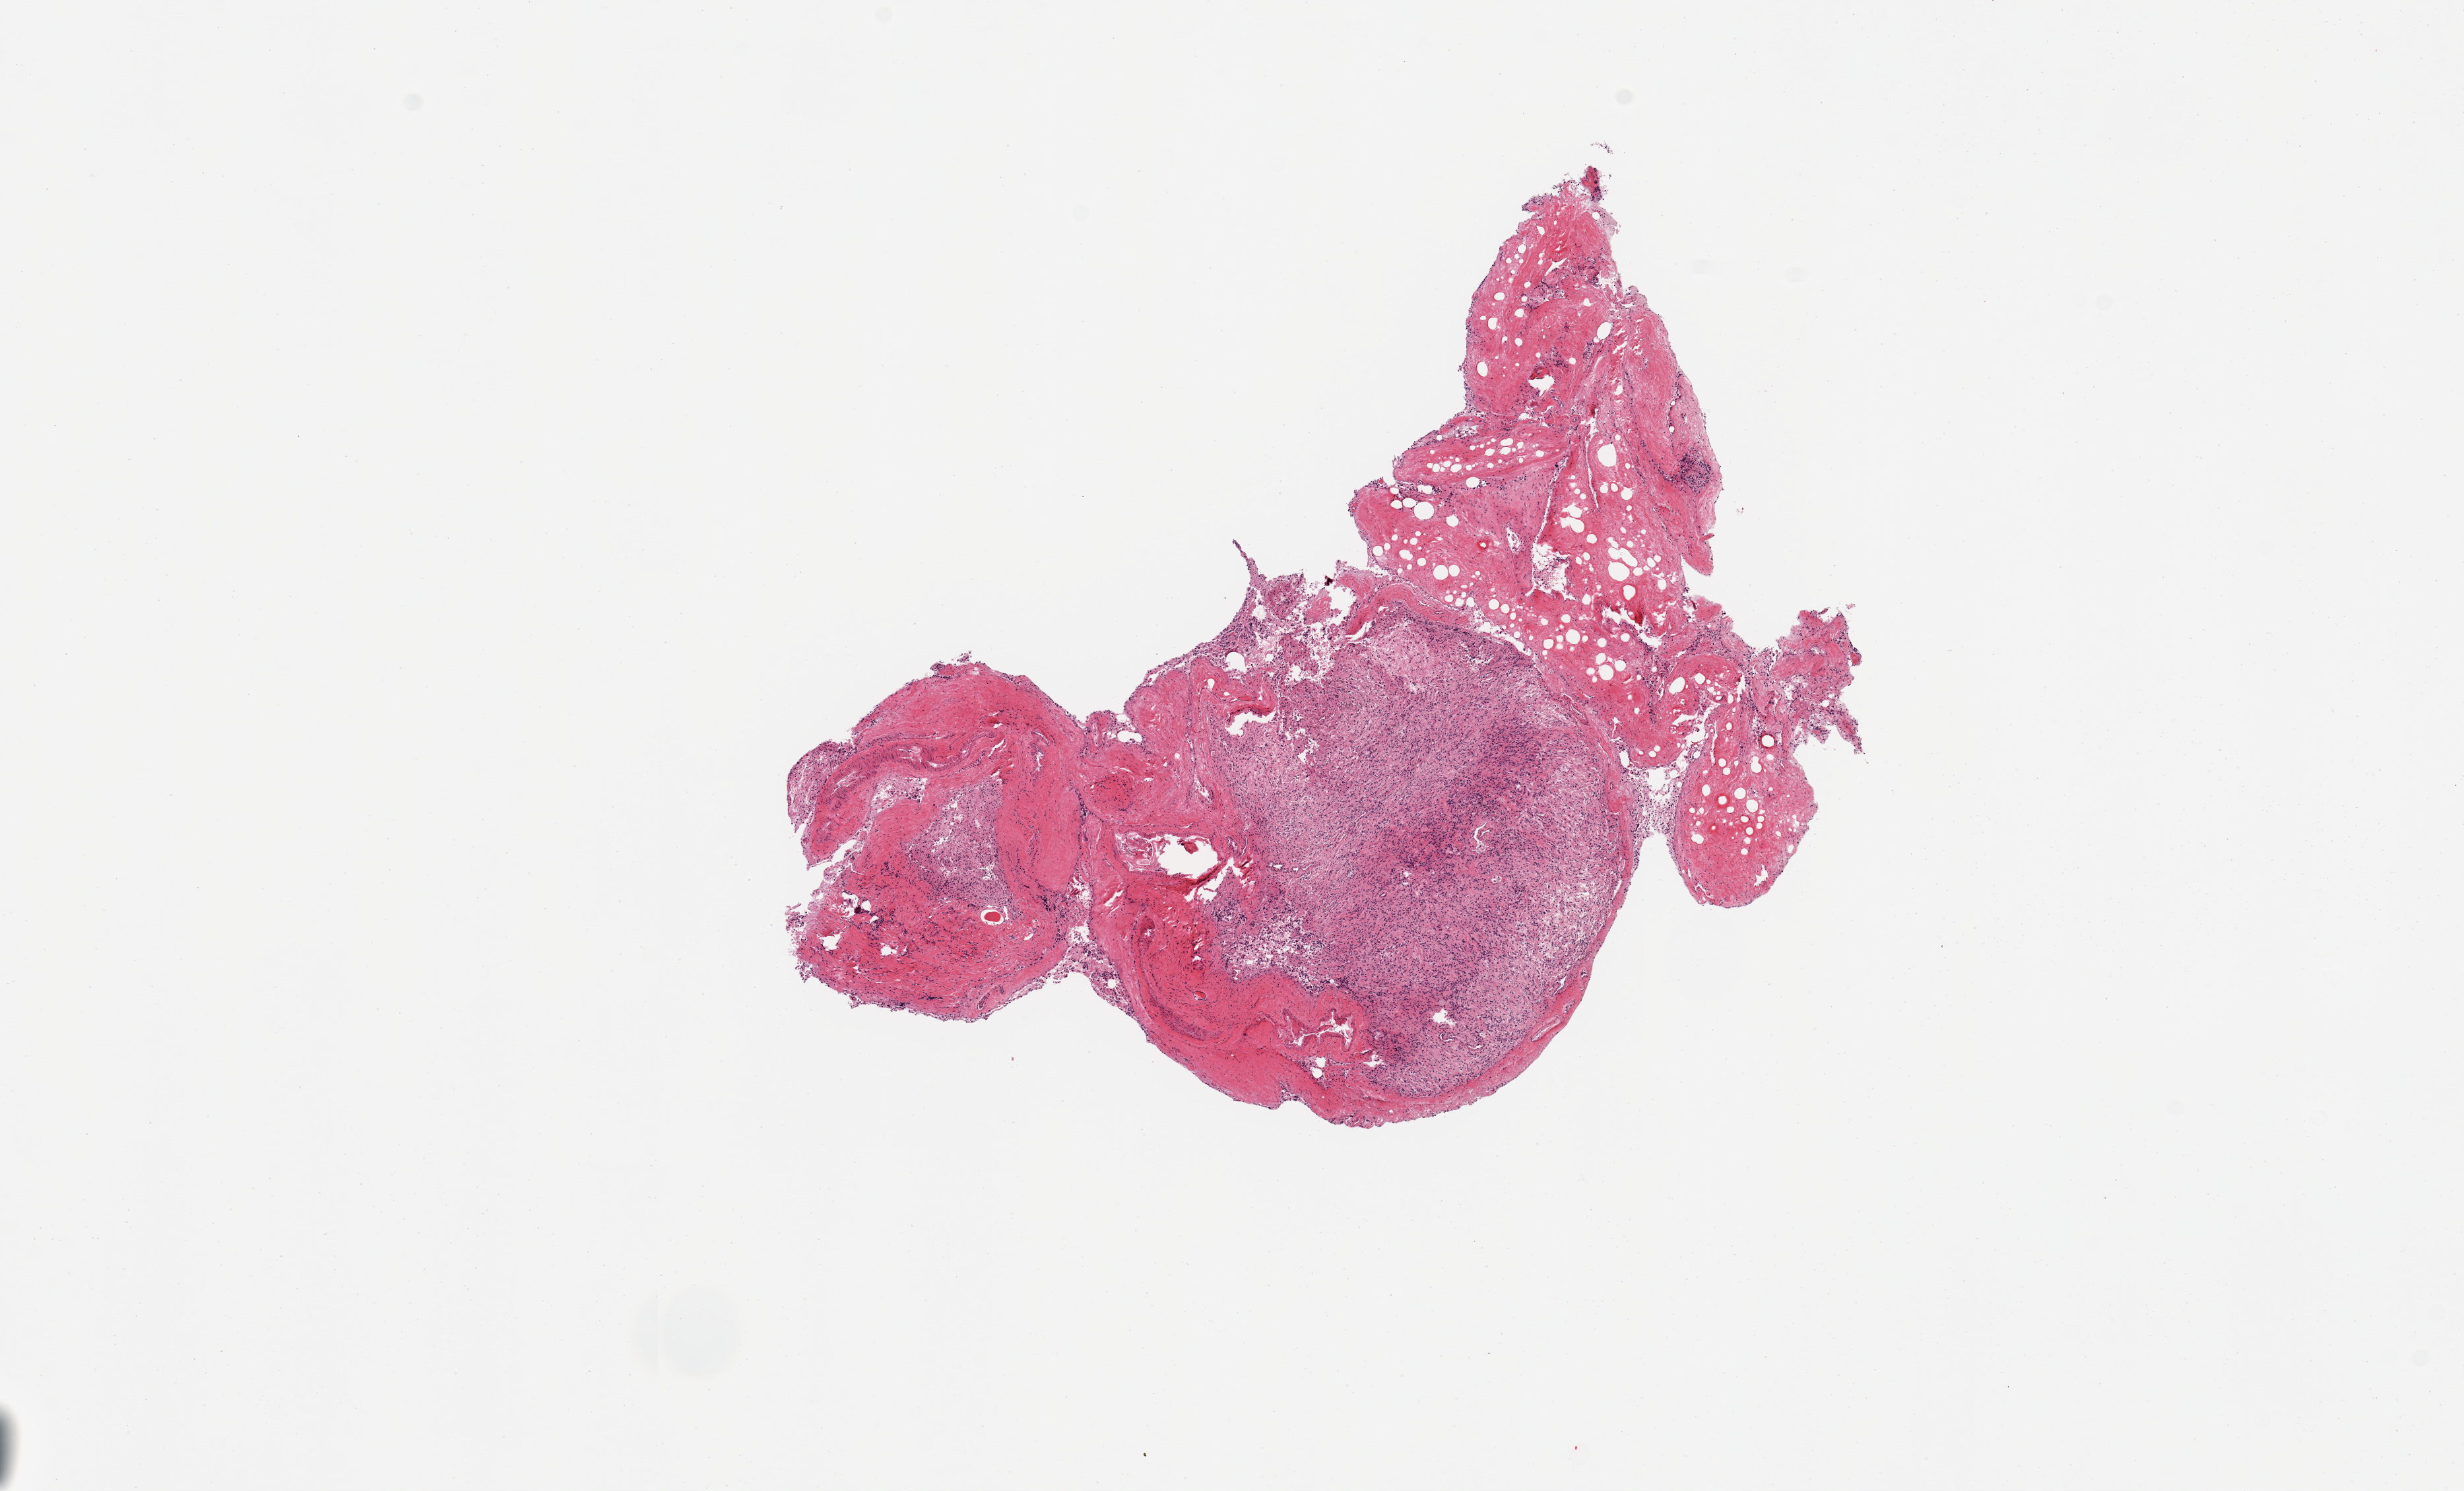
Digitized haematoxylin and eosin-stained section, low-resolution overview of the scanned area, about 14.8 x 8.9 mm (slide scanned at 20x), PAXgene-fixed, paraffin-embedded tissue, target tissue: pituitary, donor tissue sample. Donor sex: male.
Review note (as recorded): 1 piece, ~2.5x2.5mm piece adenohypophysis; rest is adherent dura.